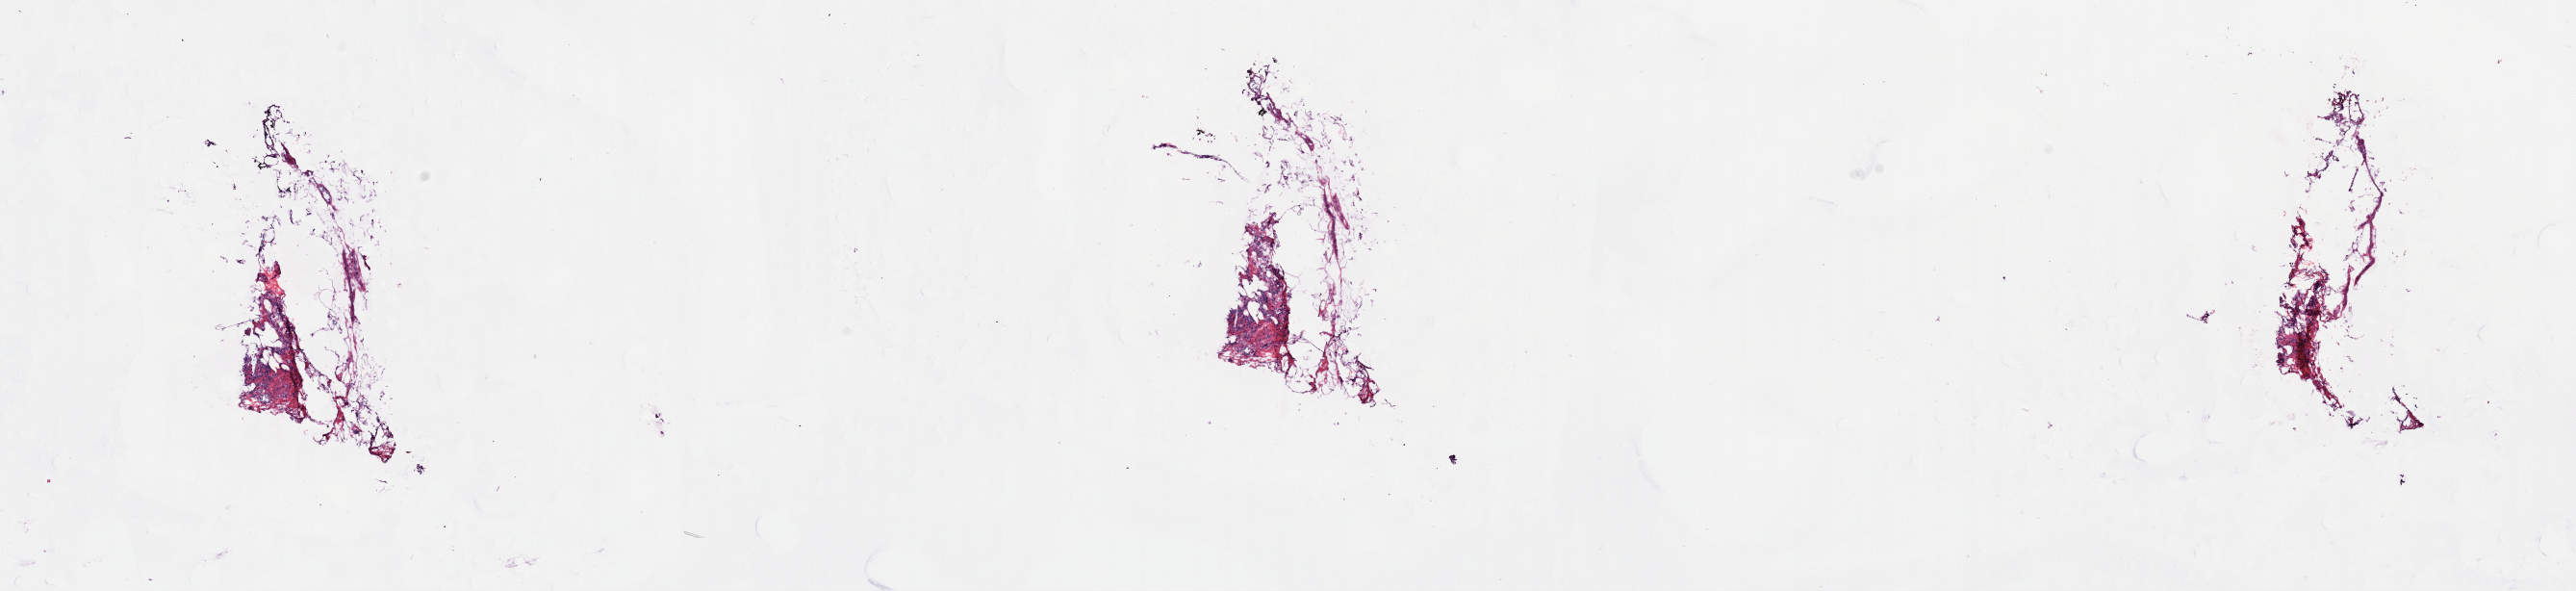
Digitized Hematoxylin and eosin (H&E) stained tissue section (whole slide), shown as a low-resolution overview of the whole scanned area (about 21.1 x 4.9 mm, slide scanned at 40x); frozen section from the top of the tissue portion; breast, primary tumour sample. Female, age 62 years at initial diagnosis. Slide review estimates, as recorded: tumour cells 35%, tumour nuclei 75%, normal cells 40%, stromal cells 25%, necrosis 0%. Infiltration values recorded for this section: lymphocyte infiltration 0%, monocyte infiltration 0%, neutrophil infiltration 0%.
* pathologic diagnosis: Lobular carcinoma, NOS
* AJCC pathologic stage: IIIC (6th edition)
* lymph nodes positive (case pathology): 18 of 18 examined